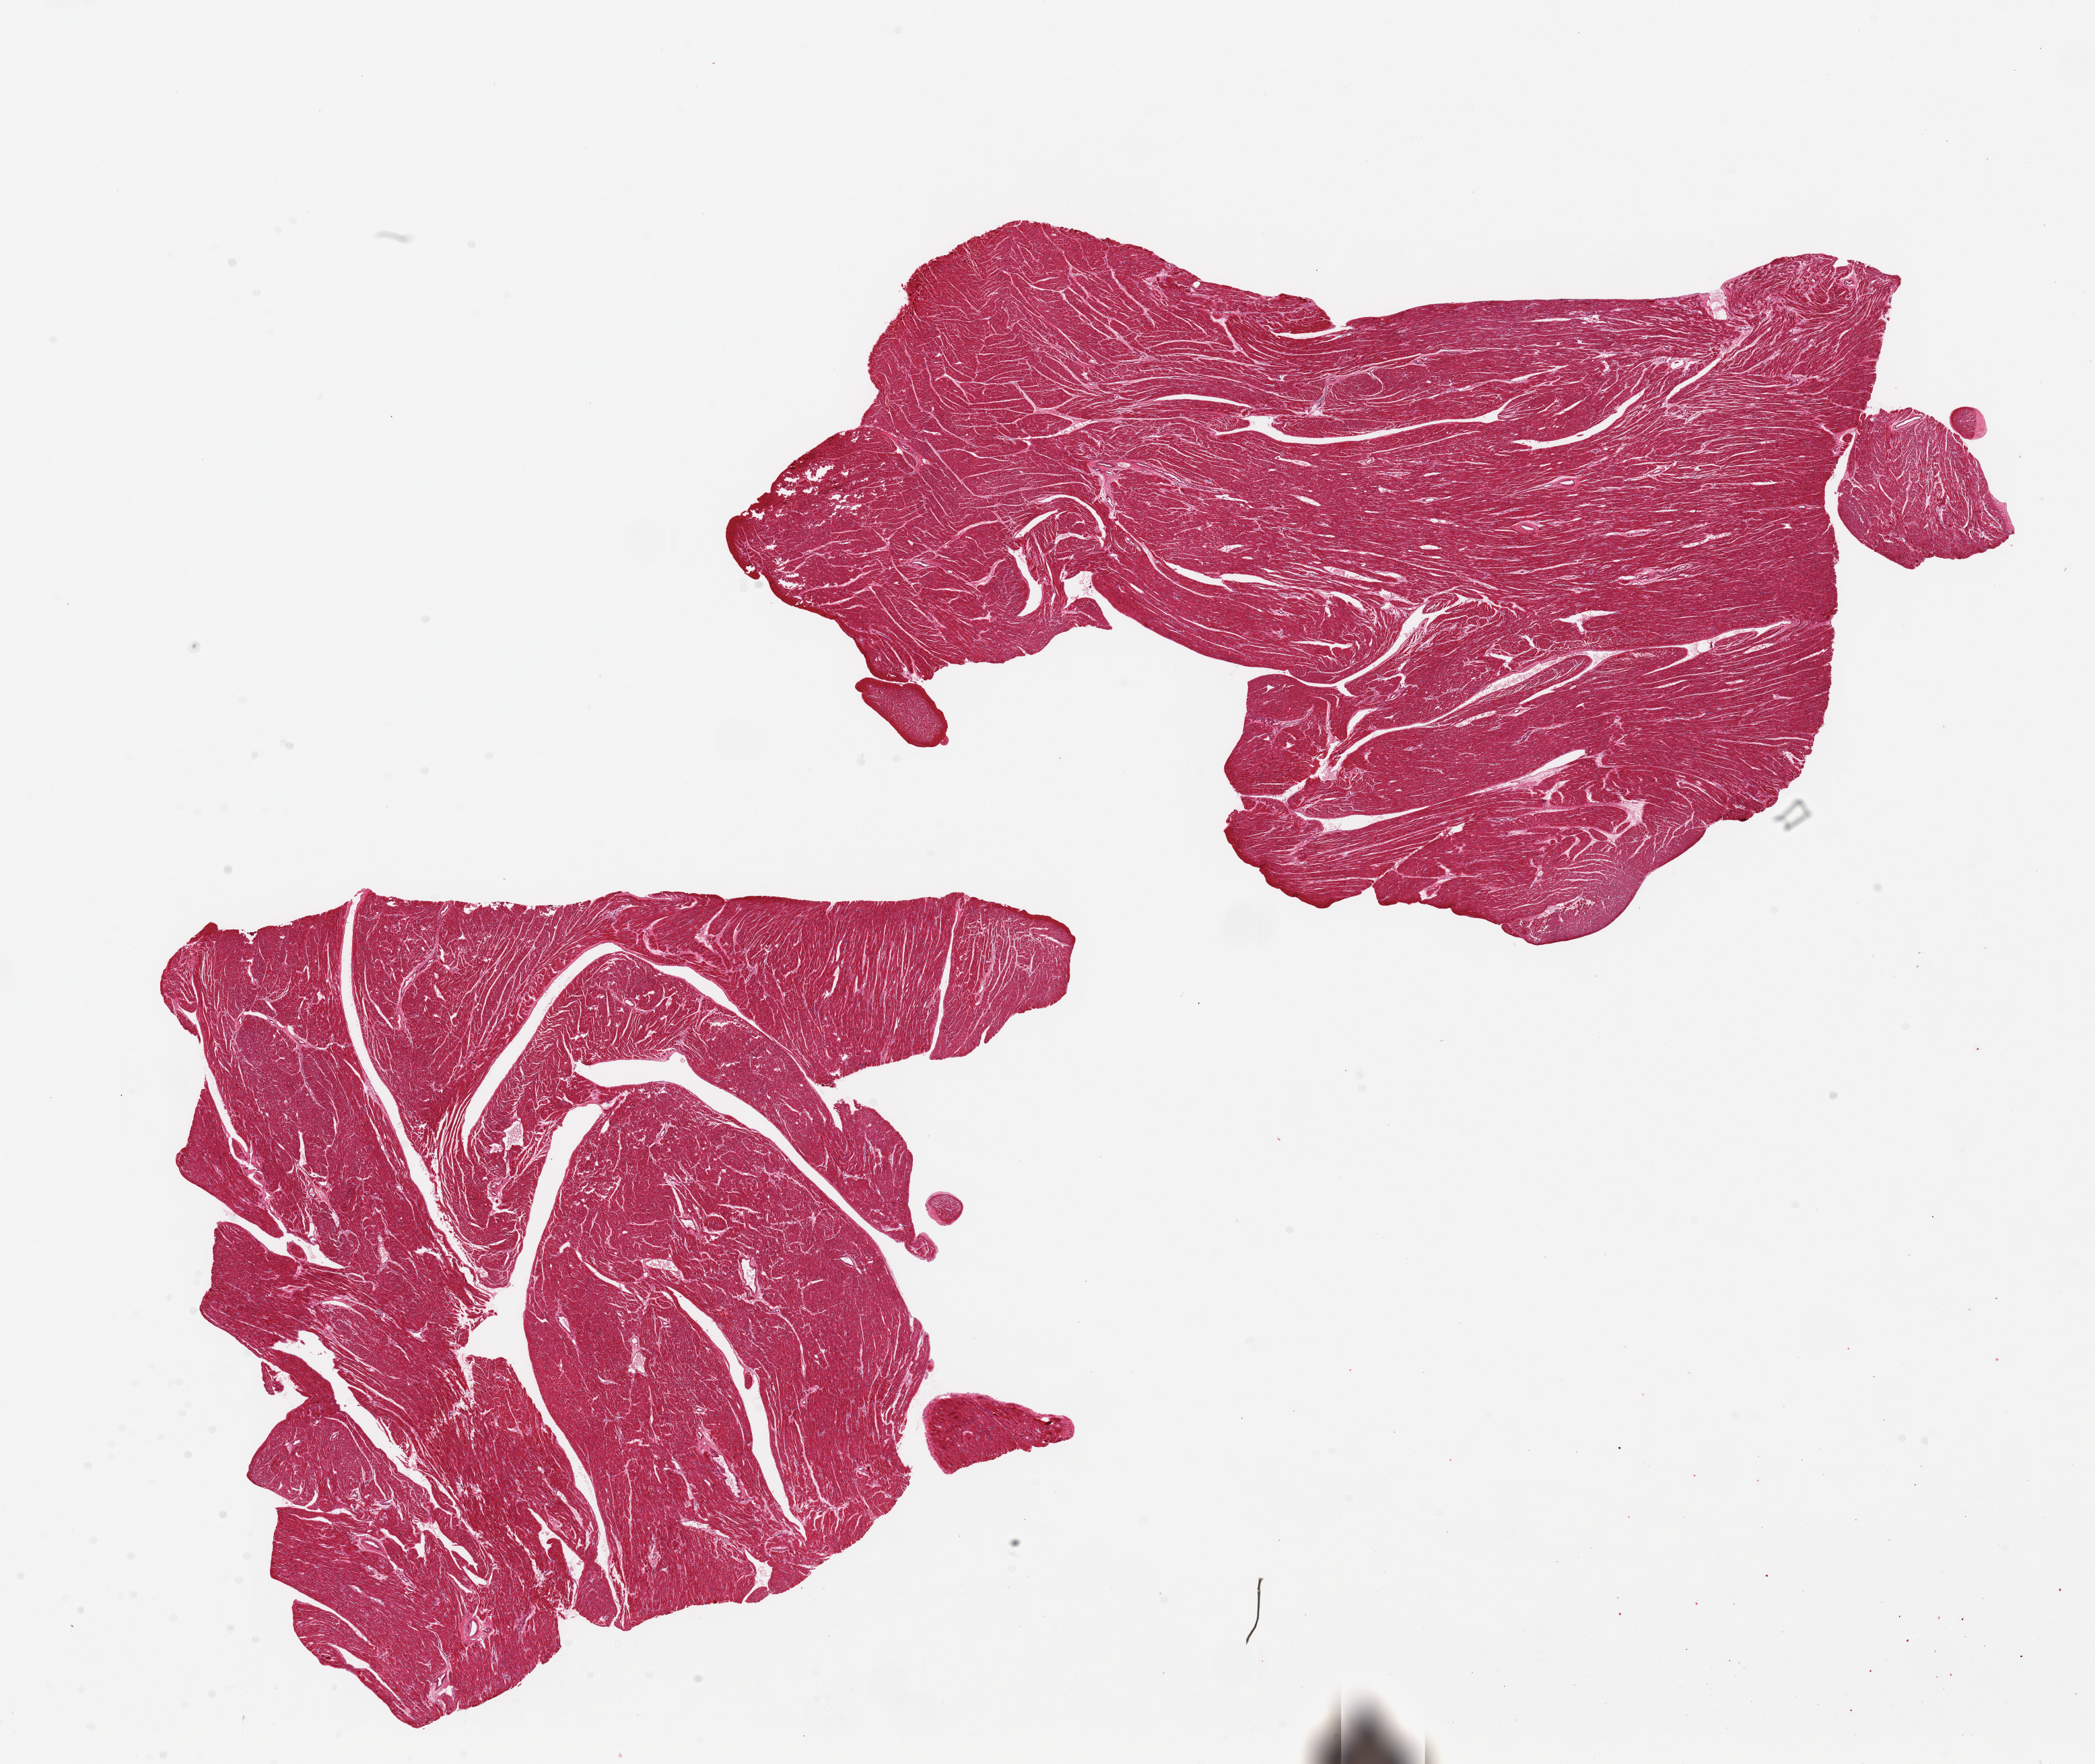
Digitized haematoxylin and eosin-stained section, brightfield — shown as a low-resolution overview of the whole scanned area (about 24.6 x 20.7 mm), PAXgene-fixed paraffin-embedded (PFPE) section, section of heart (target tissue), donor tissue sample. Female donor.
- reviewer comment on this tissue sample: 2 pieces 13x7 & 10x10 mm; no adipose